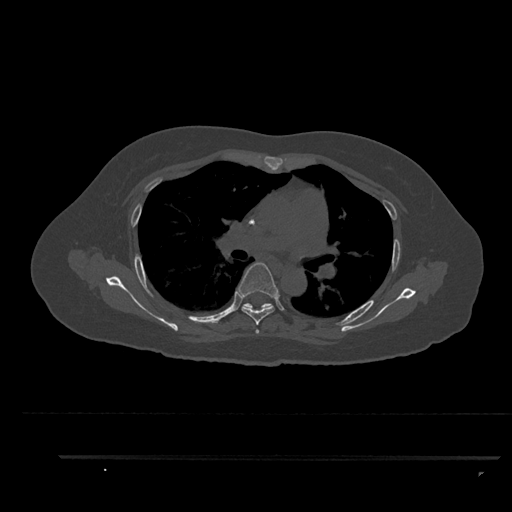
CT including the spine, one axial slice; bone window (W 1800 / L 400 HU); 512 × 512 image matrix, field of view 408 × 408 mm. Female patient, age 44 years. From the clinical record (not read from this slice): primary cancer: renal; vertebrae with lytic lesions (as recorded): L1.
Outlined on this slice (semi-automatically segmented with operator editing):
- T4 vertebra: bounding box <255,329,259,334> (left, top, right, bottom; pixels)
- T5 vertebra: <238,262,278,325>
- T6 vertebra: <242,303,273,310>